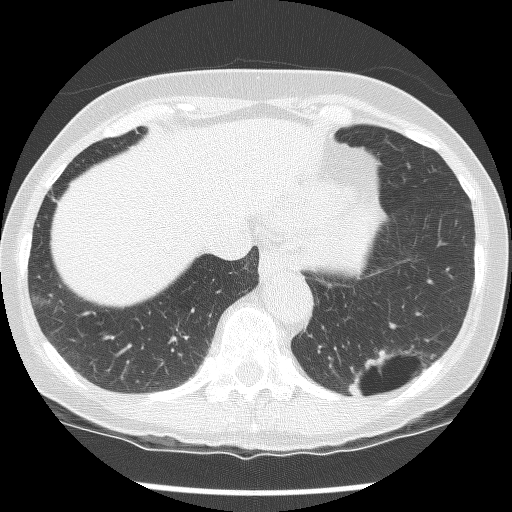
Low-dose screening chest CT, axial slice. Second annual screen. Lung window (W 1500 / L -600 HU). 2.5 mm slice thickness. Slice 101 of 136 in the series. Female participant, aged 61 years at enrolment.
Lesion marked by an expert reader, bounding box (x1, y1, x2, y2) in pixels: (328, 314, 439, 413). The screening reader recorded 2 non-calcified nodules or masses ≥4 mm on this exam; which of them this box marks is not recorded. Official screen result: positive, no significant change: stable abnormalities potentially related to lung cancer, unchanged since the prior screening exam. Participant outcome: lung cancer diagnosed 585 days after this screen (after the third annual screen) — non-small cell carcinoma, left lower lobe, poorly differentiated (G3), stage IB (AJCC 6th edition), 100 mm at pathology.